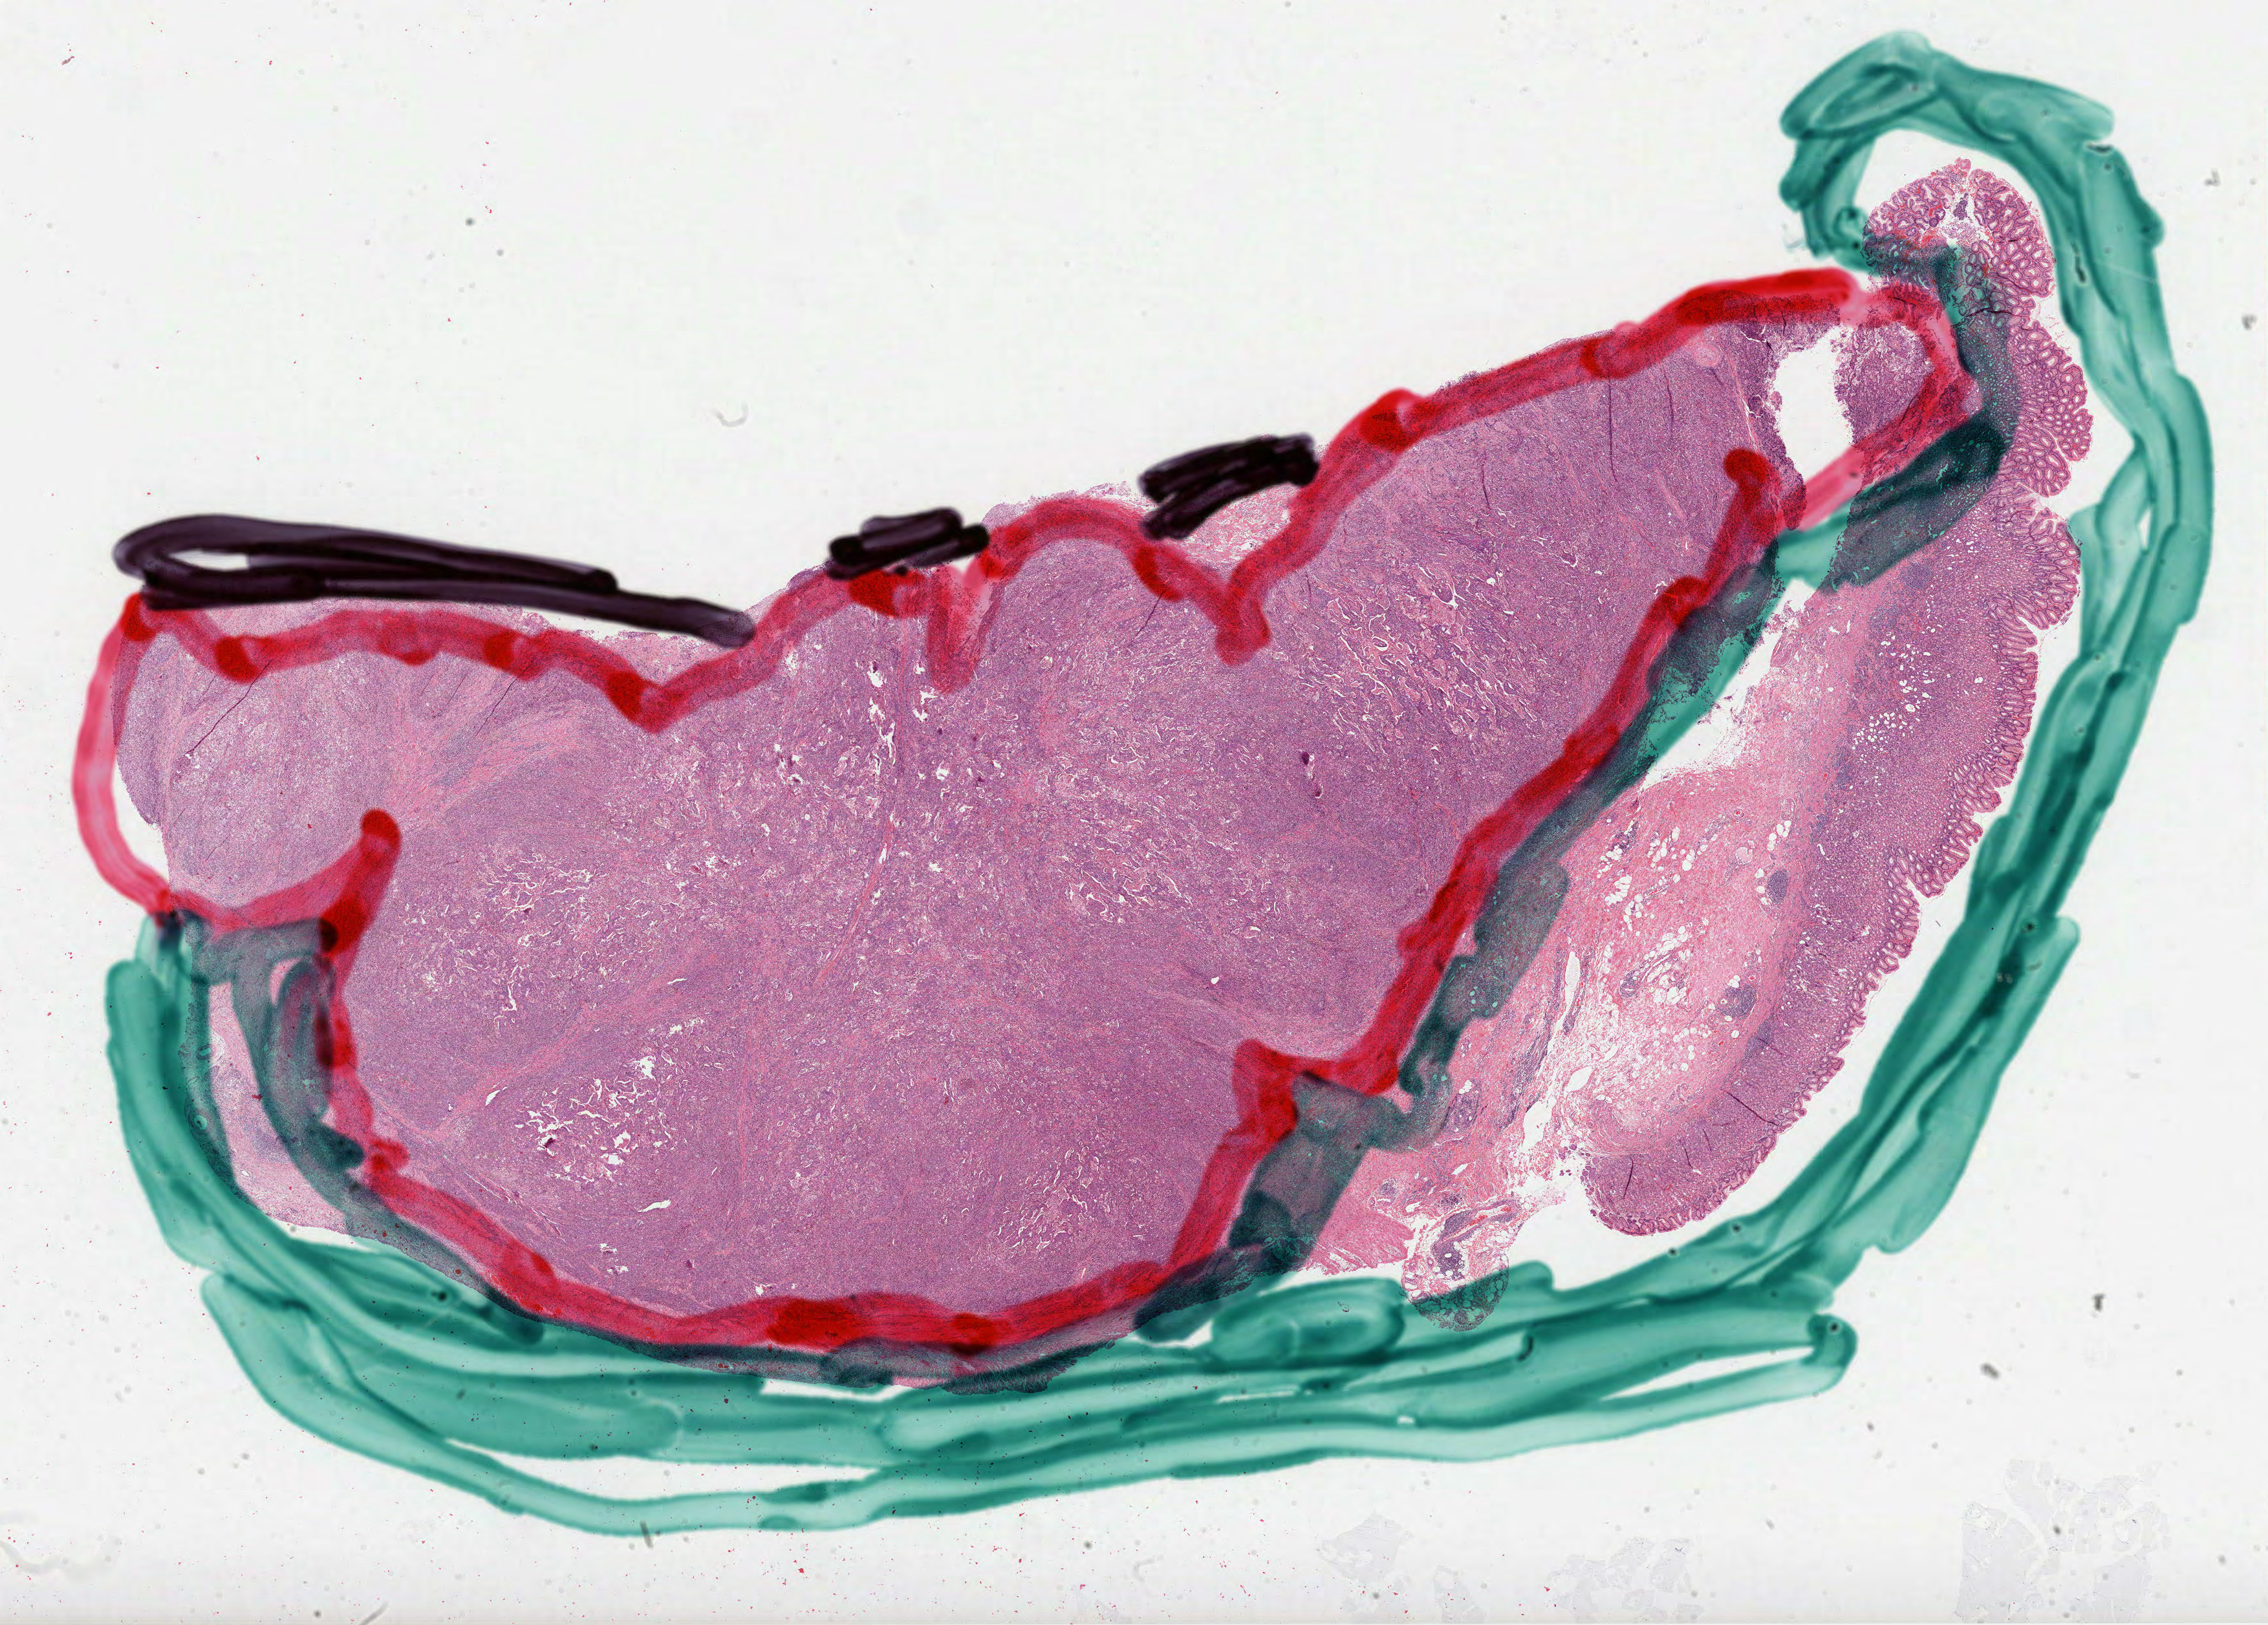
Whole-slide histology image, Hematoxylin and eosin (H&E) stained — shown as a low-resolution overview of the whole scanned area (about 28.3 x 20.3 mm). Formalin-fixed paraffin-embedded (FFPE) diagnostic section. Sample: primary tumour, stomach. Male, age 65 years at initial diagnosis.
Diagnosis: Adenocarcinoma, NOS.